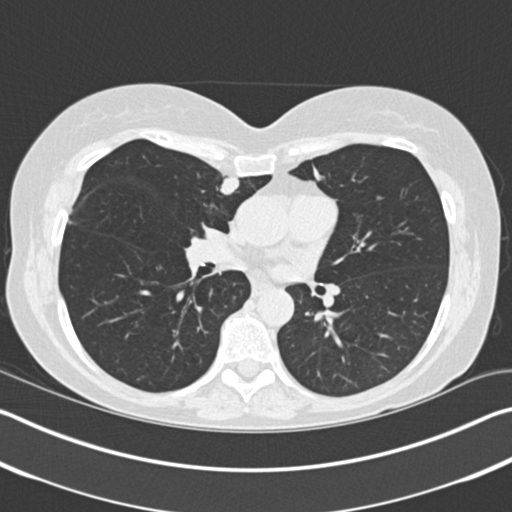
Low-dose screening chest CT, one axial slice. Position 97 of 183 along the scan axis. Reconstruction kernel B30f. 120 kVp. Lung window (W 1500 / L -600 HU). 2 mm slice thickness. 512 × 512 image matrix.
Structures marked on this image (manually delineated by an expert):
- lesion 1 (tumor, upper lobe of right lung): bounding box (x1, y1, x2, y2) in pixels: (220, 176, 239, 195)